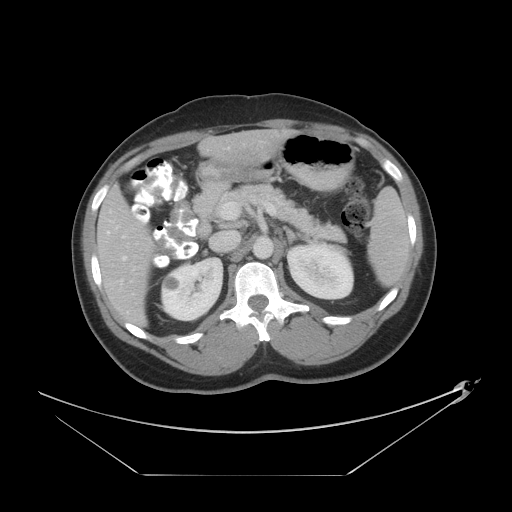
Contrast-enhanced abdominal CT, one axial slice; position 23 of 44 along the scan axis; reconstruction kernel STANDARD; 120 kVp; intravenous contrast given; soft-tissue window (W 400 / L 40 HU); 512 × 512 image matrix, field of view 466 × 466 mm. Male patient, age 49 years. Case-level facts recorded for this patient, not image findings: diagnosis: colorectal cancer liver metastases, imaged before liver resection; multiple liver metastases: no; largest metastasis: 8.5 cm; disease in both lobes: yes.
Structures marked on this image (expert manual segmentation):
- hepatic veins: bounding box <122,148,229,266> (left, top, right, bottom; pixels)
- liver: <97,130,295,327>
- planned liver remnant (the part of the liver to remain after resection): <225,130,295,163>
- portal vein (with intrahepatic branches): <107,231,124,238>